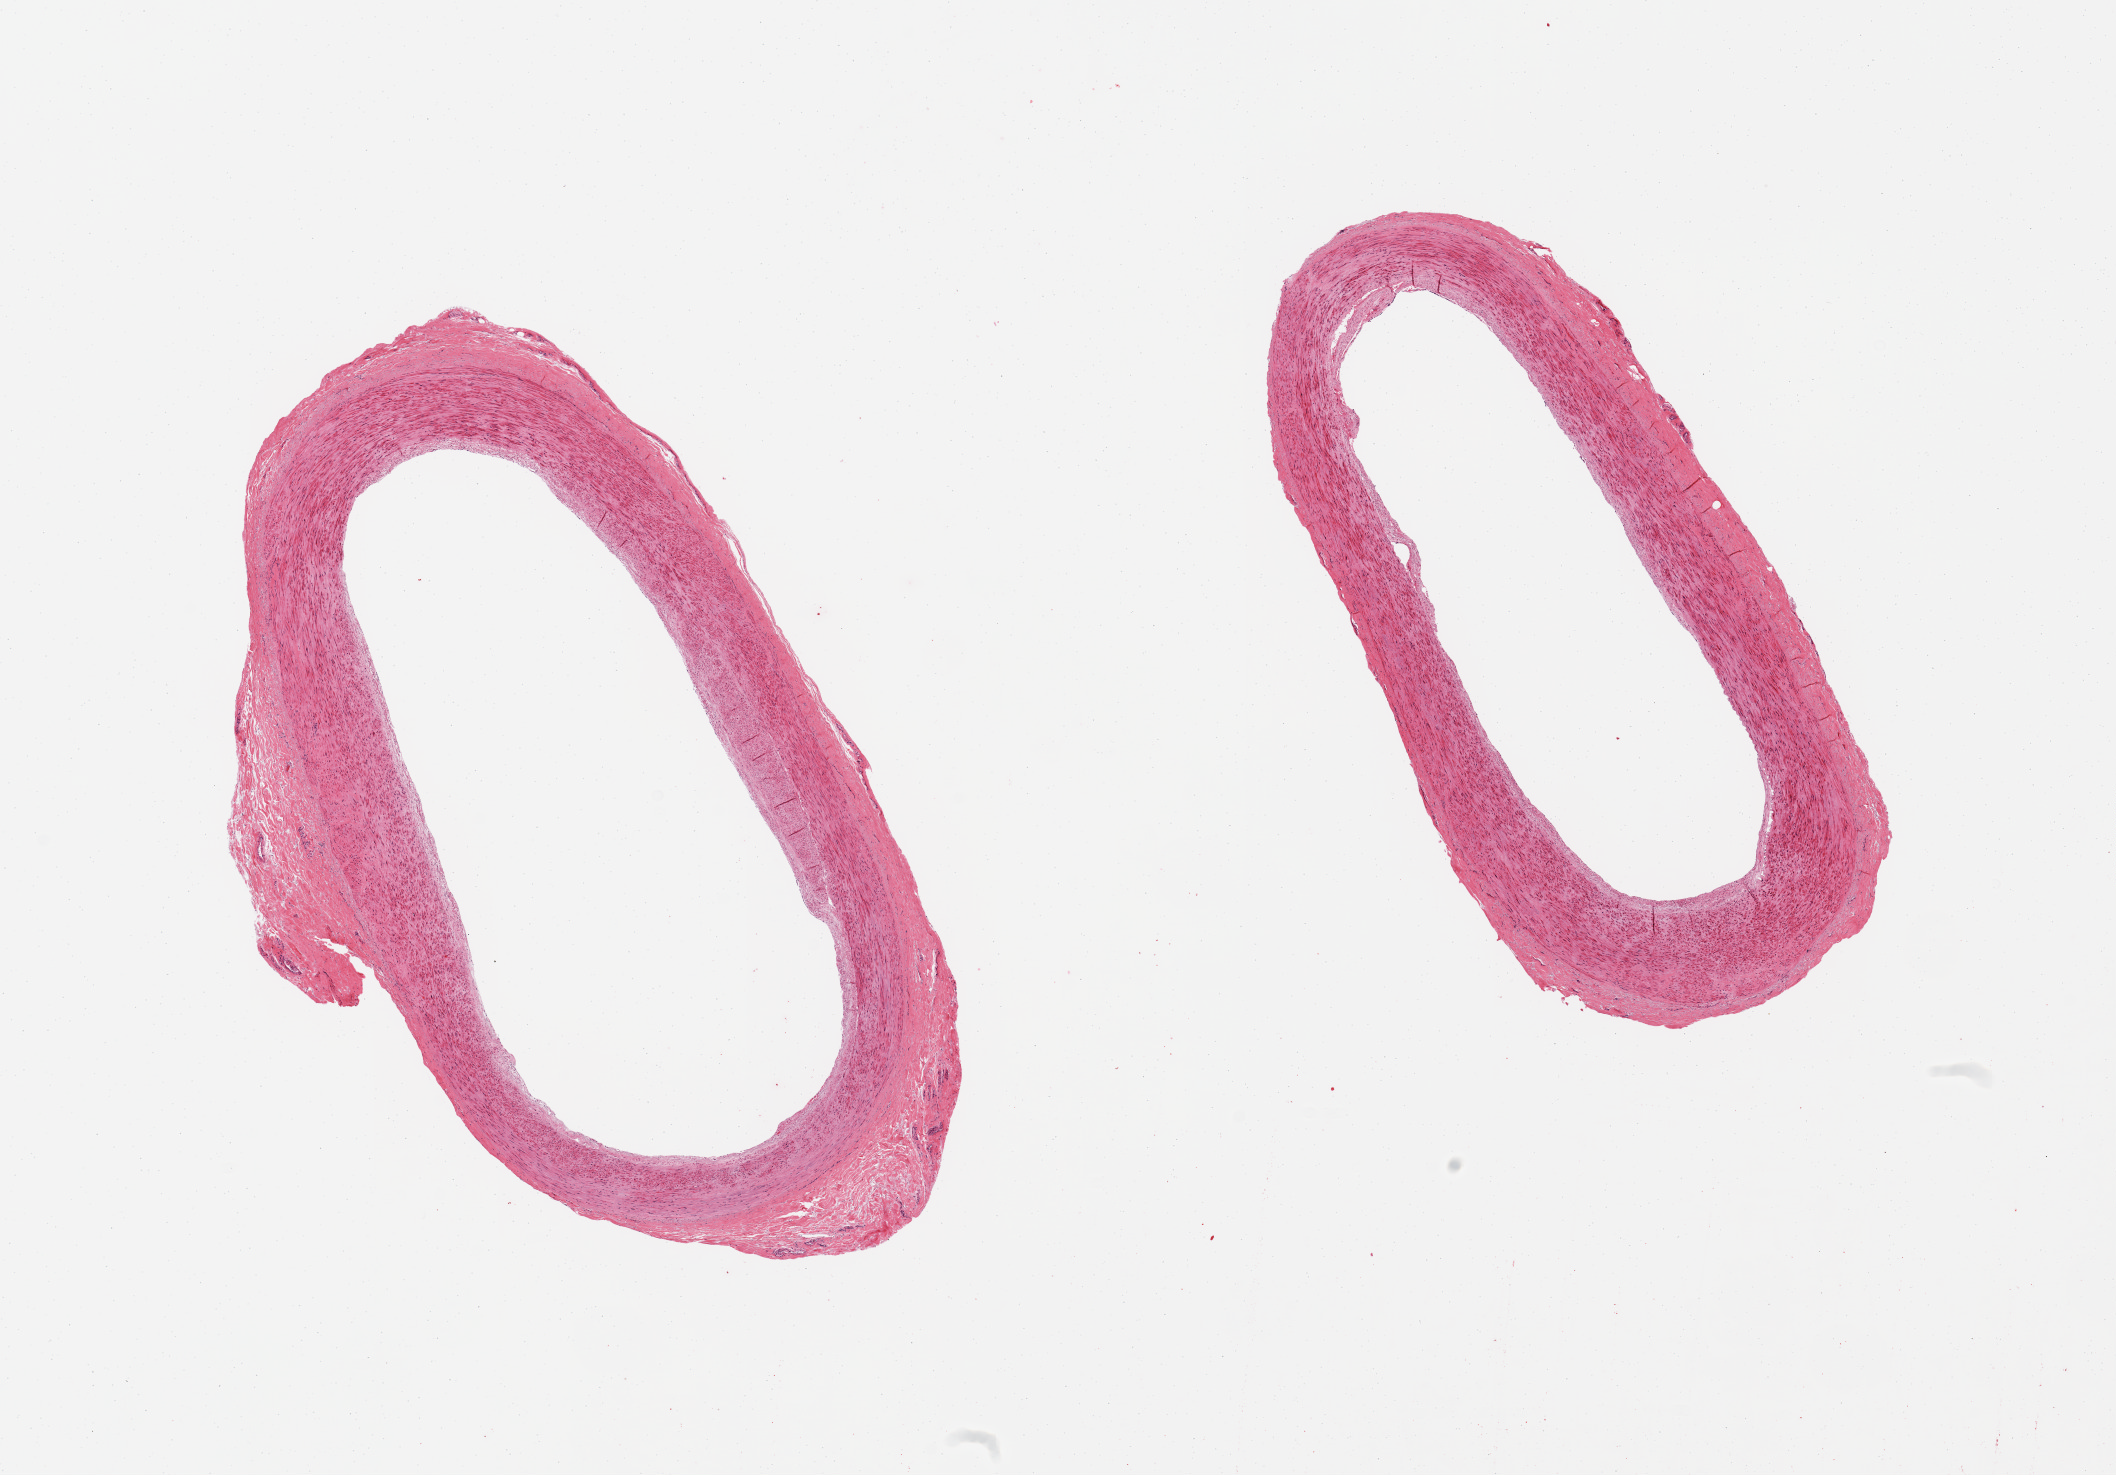
Digitized hematoxylin and eosin (H&E)-stained section — shown as a low-resolution overview of the whole scanned area (about 16.7 x 11.7 mm); PAXgene-fixed paraffin-embedded (PFPE) section; section of tibial artery (target tissue); tissue donor sample. Donor: male.
Review note (as recorded): 2 pieces, well trimmed.